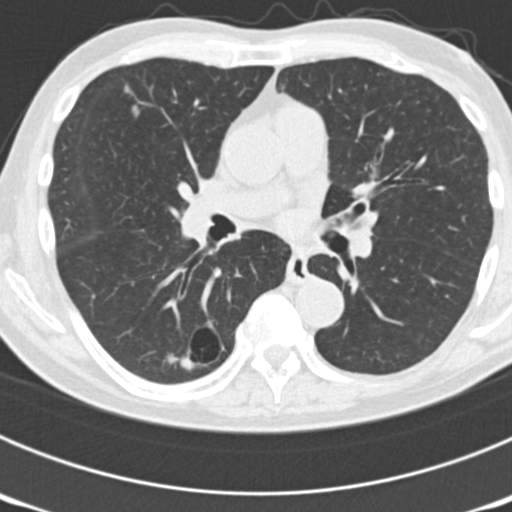
Axial slice from a low-dose chest CT screening exam; third annual screen; lung window (W 1500 / L -600 HU); standard (soft-tissue) reconstruction kernel (B30f). Male participant, aged 70 years at enrolment. Current smoker at enrolment.
Expert reader's lesion annotation, bounding box <146,305,238,385> (left, top, right, bottom; pixels). The screening reader recorded 3 non-calcified nodules or masses ≥4 mm on this exam; which of them this box marks is not recorded. Official screen result: positive, other.